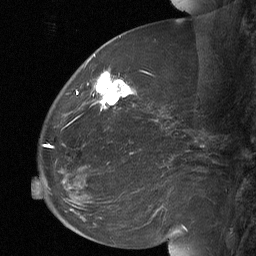
Breast MRI (dynamic contrast-enhanced), one sagittal slice; slice 26 of 64 in the series (ordered by position); dynamic contrast-enhanced study with each time point stored as its own series, time point 2 of 3 at this slice position (early post-contrast, ordered by acquisition time); 1.5 T; TE 4.8 ms, TR 27 ms; 256 × 256 image matrix, field of view 200 × 200 mm. Patient: female, 60 years. Case-level facts recorded for this patient, not image findings: setting: breast cancer imaged before/during neoadjuvant chemotherapy; receptor status: HR-positive, HER2-negative.
Annotated regions visible in this slice (semi-automatic segmentation, software-assisted and operator-edited):
- analysis volume of interest (the breast-tissue region the enhancement analysis was run in; not a lesion): bounding box [x1, y1, x2, y2] px = [92, 70, 134, 112]
- tumour enhancement mask (voxels above the 90 % enhancement threshold inside the analysis volume of interest): [96, 72, 131, 105]